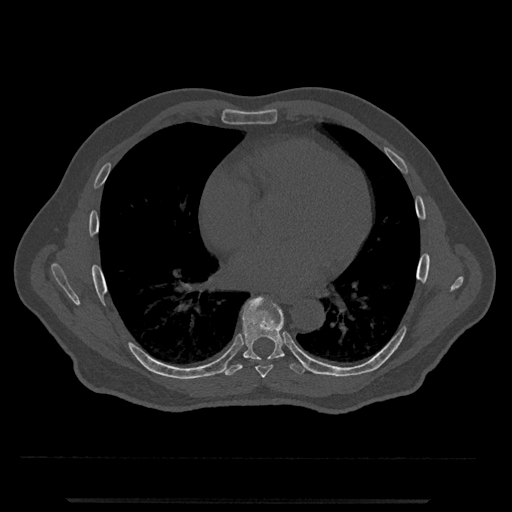
CT including the spine, one axial slice; slice 652 of 797 in the series (ordered by position); 120 kVp; bone window (W 1800 / L 400 HU); 0.5 mm slice thickness; 512 × 512 image matrix, field of view 419 × 419 mm. Patient: male, 63 years. From the clinical record (not read from this slice): primary cancer: prostate.
Annotated regions visible in this slice (semi-automatic segmentation, software-assisted and operator-edited):
- T7 vertebra: bounding box <256,365,273,379> (left, top, right, bottom; pixels)
- T8 vertebra: <225,296,305,376>